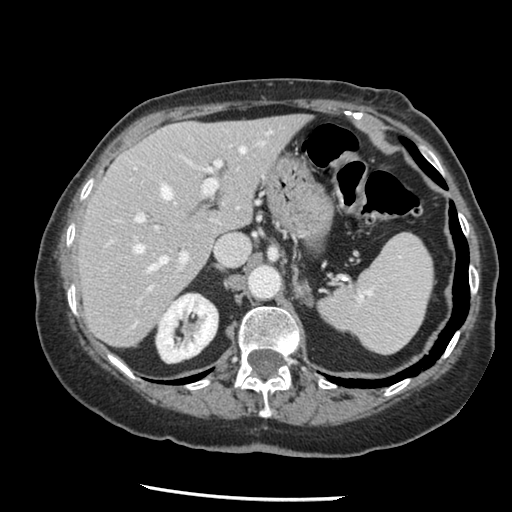
Contrast-enhanced abdominal CT, one axial slice. Reconstruction kernel STANDARD. 120 kVp. Intravenous contrast given. Soft-tissue window (W 400 / L 40 HU). 2.5 mm slice thickness. 512 × 512 image matrix. Female patient, age 85 years. Case-level facts recorded for this patient, not image findings: diagnosis: colorectal cancer liver metastases, imaged before liver resection; multiple liver metastases: no; largest metastasis: 0.9 cm; disease in both lobes: no.
Structures marked on this image (outlined manually by an expert reader):
- hepatic veins: bounding box (x1, y1, x2, y2) in pixels: (134, 134, 269, 271)
- liver: (79, 117, 307, 347)
- planned liver remnant (the part of the liver to remain after resection): (79, 117, 307, 347)
- portal vein (with intrahepatic branches): (110, 145, 230, 290)